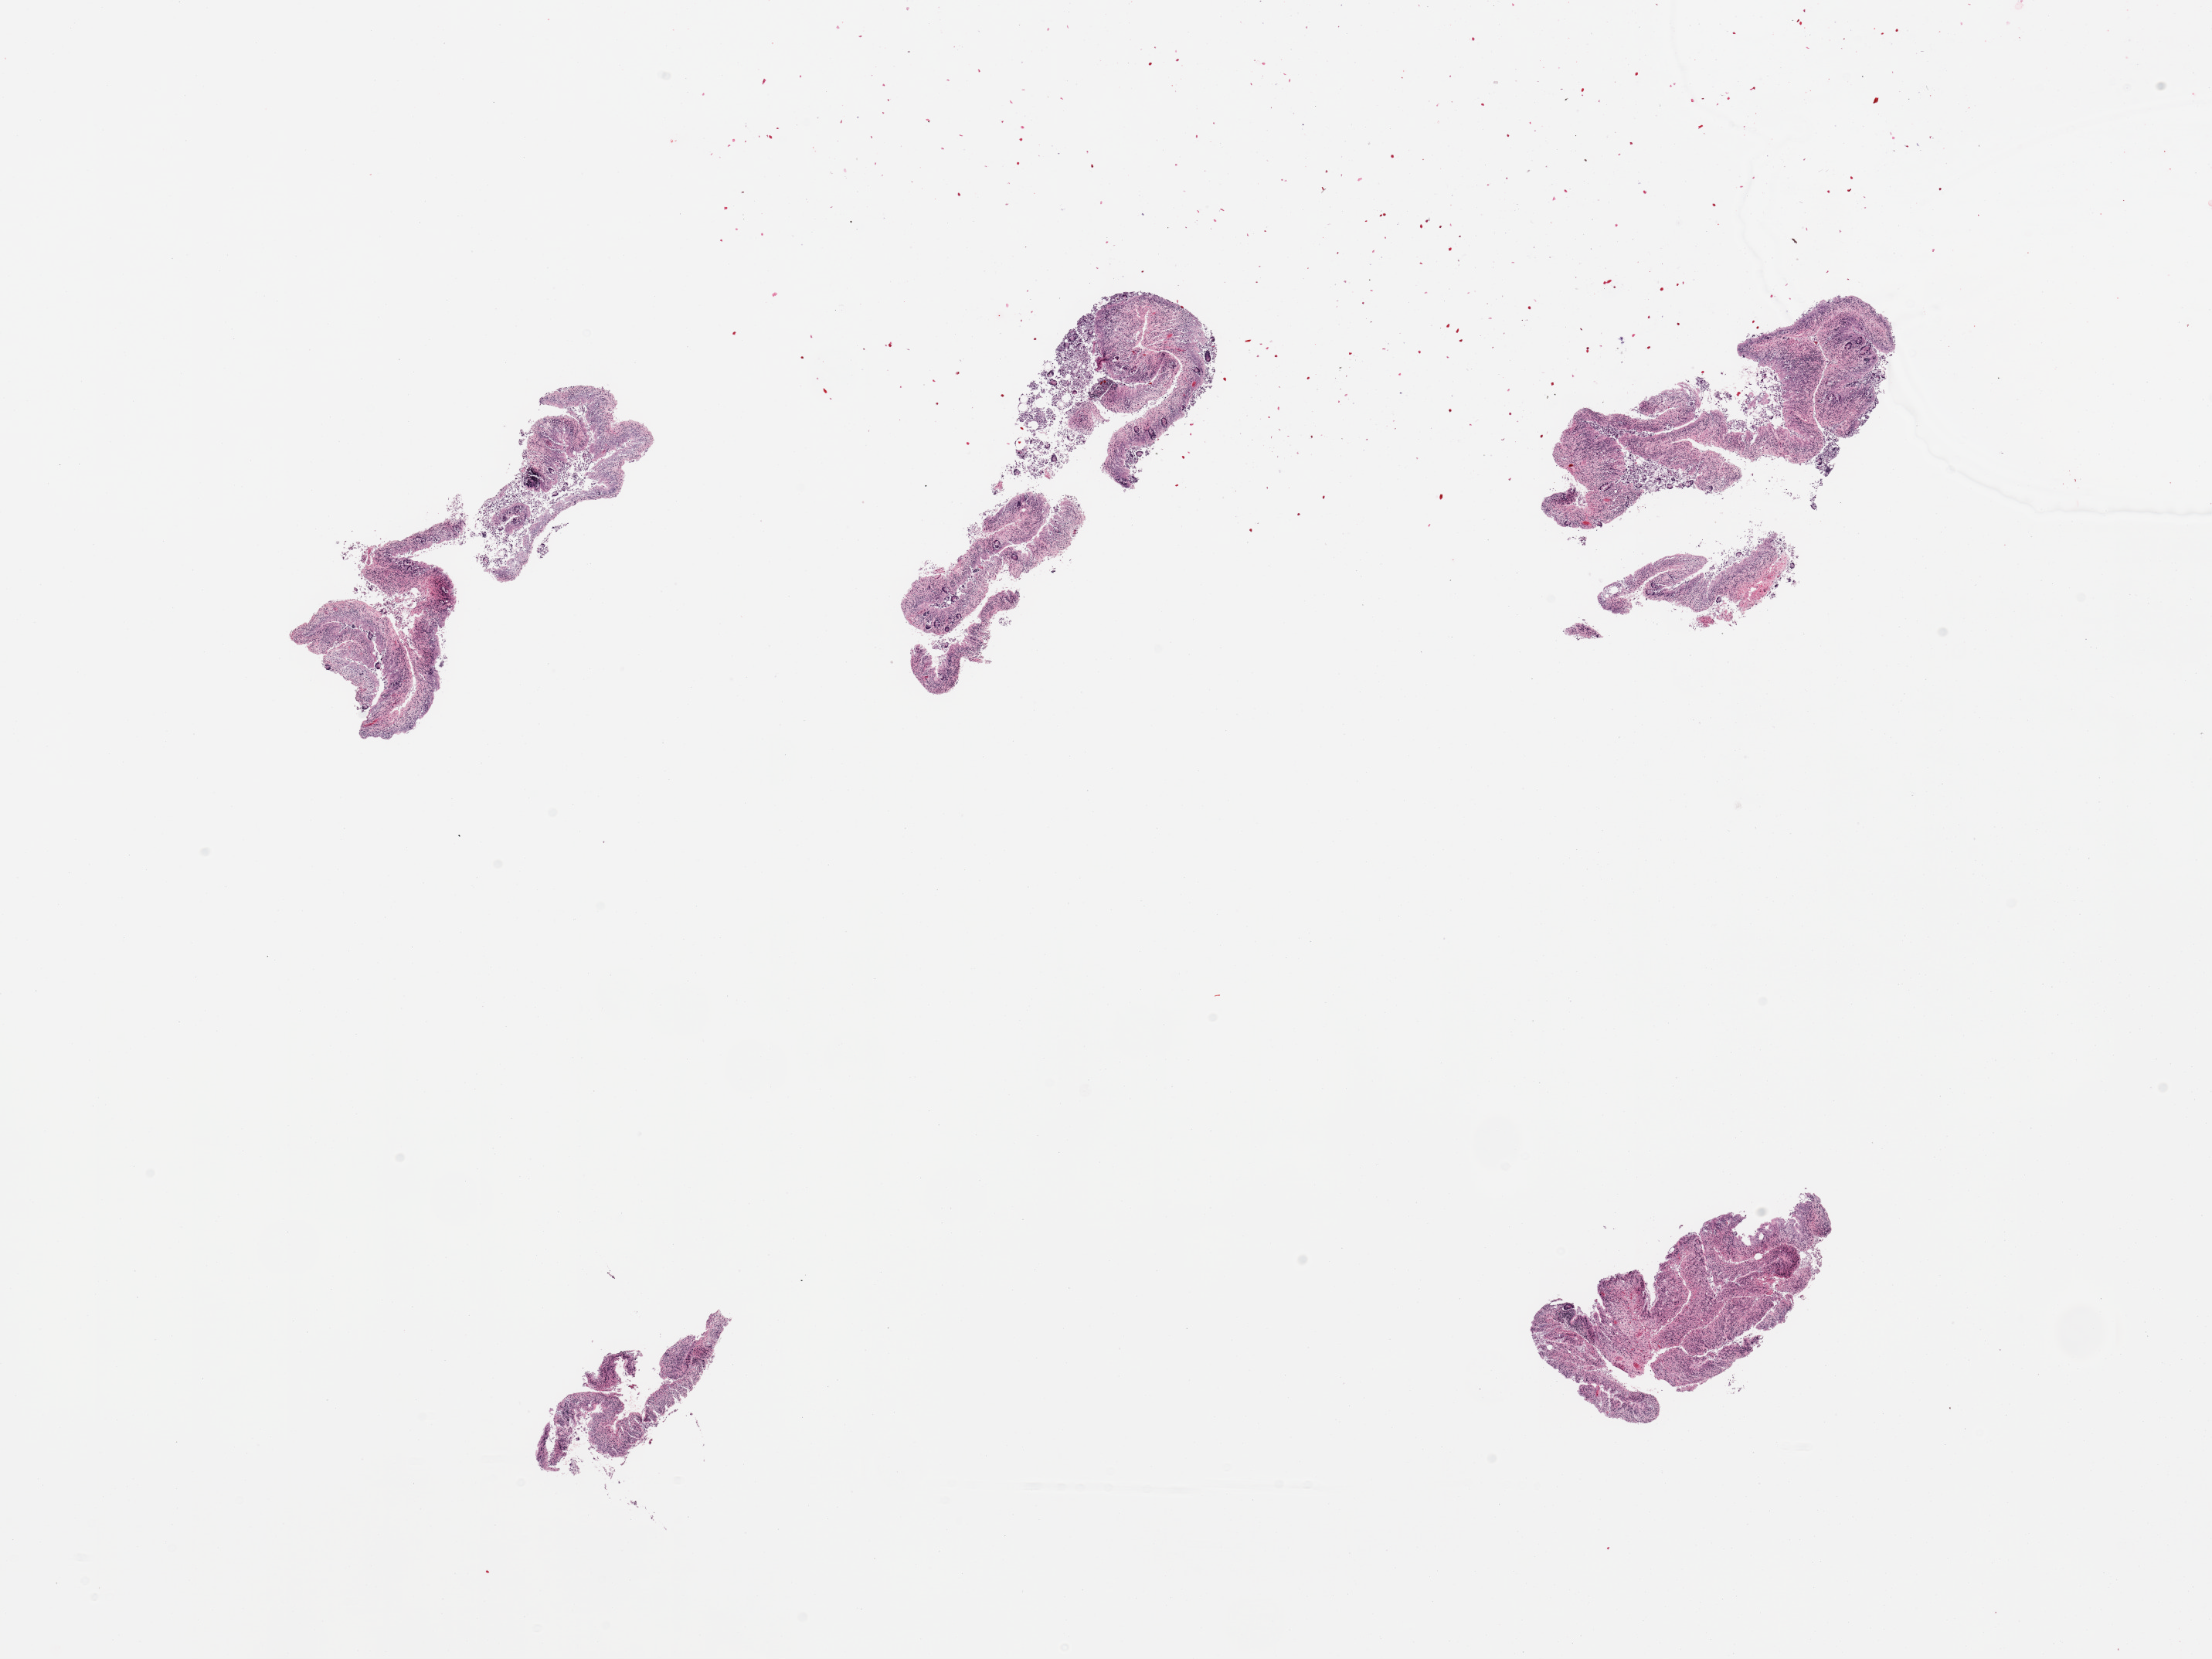
Whole-slide image, hematoxylin and eosin (H&E) stain, low-resolution overview of the scanned area, about 22.6 x 17.0 mm, PAXgene-fixed, paraffin-embedded tissue, sampled site (target tissue): ileum, donor tissue sample. Donor: male.
Review note (as recorded): 6 pieces; well dissected mucosa, but no lymphoid tissue.